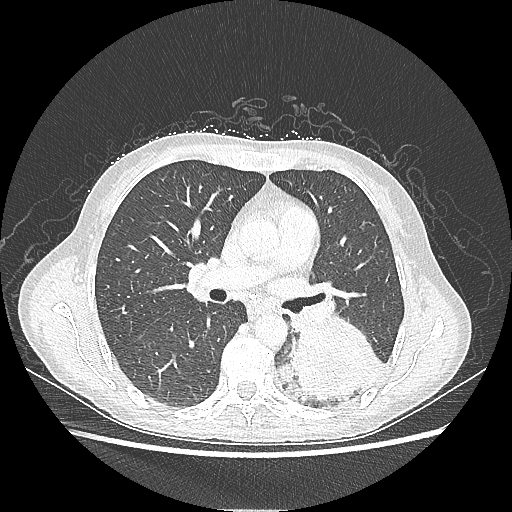
Chest CT, one axial slice. Position 124 of 220 along the scan axis. Reconstruction kernel LUNG. 80 kVp. Lung window (W 1500 / L -600 HU). 512 × 512 image matrix, field of view 360 × 360 mm. Female patient, age 53 years. Case-level facts recorded for this patient, not image findings: clinical TNM (as recorded): T3 N0 M0.
Structures marked on this image (bounding box drawn by a radiologist):
- lung tumour (recorded histology: adenocarcinoma): box from (x=276, y=318) to (x=381, y=405) px